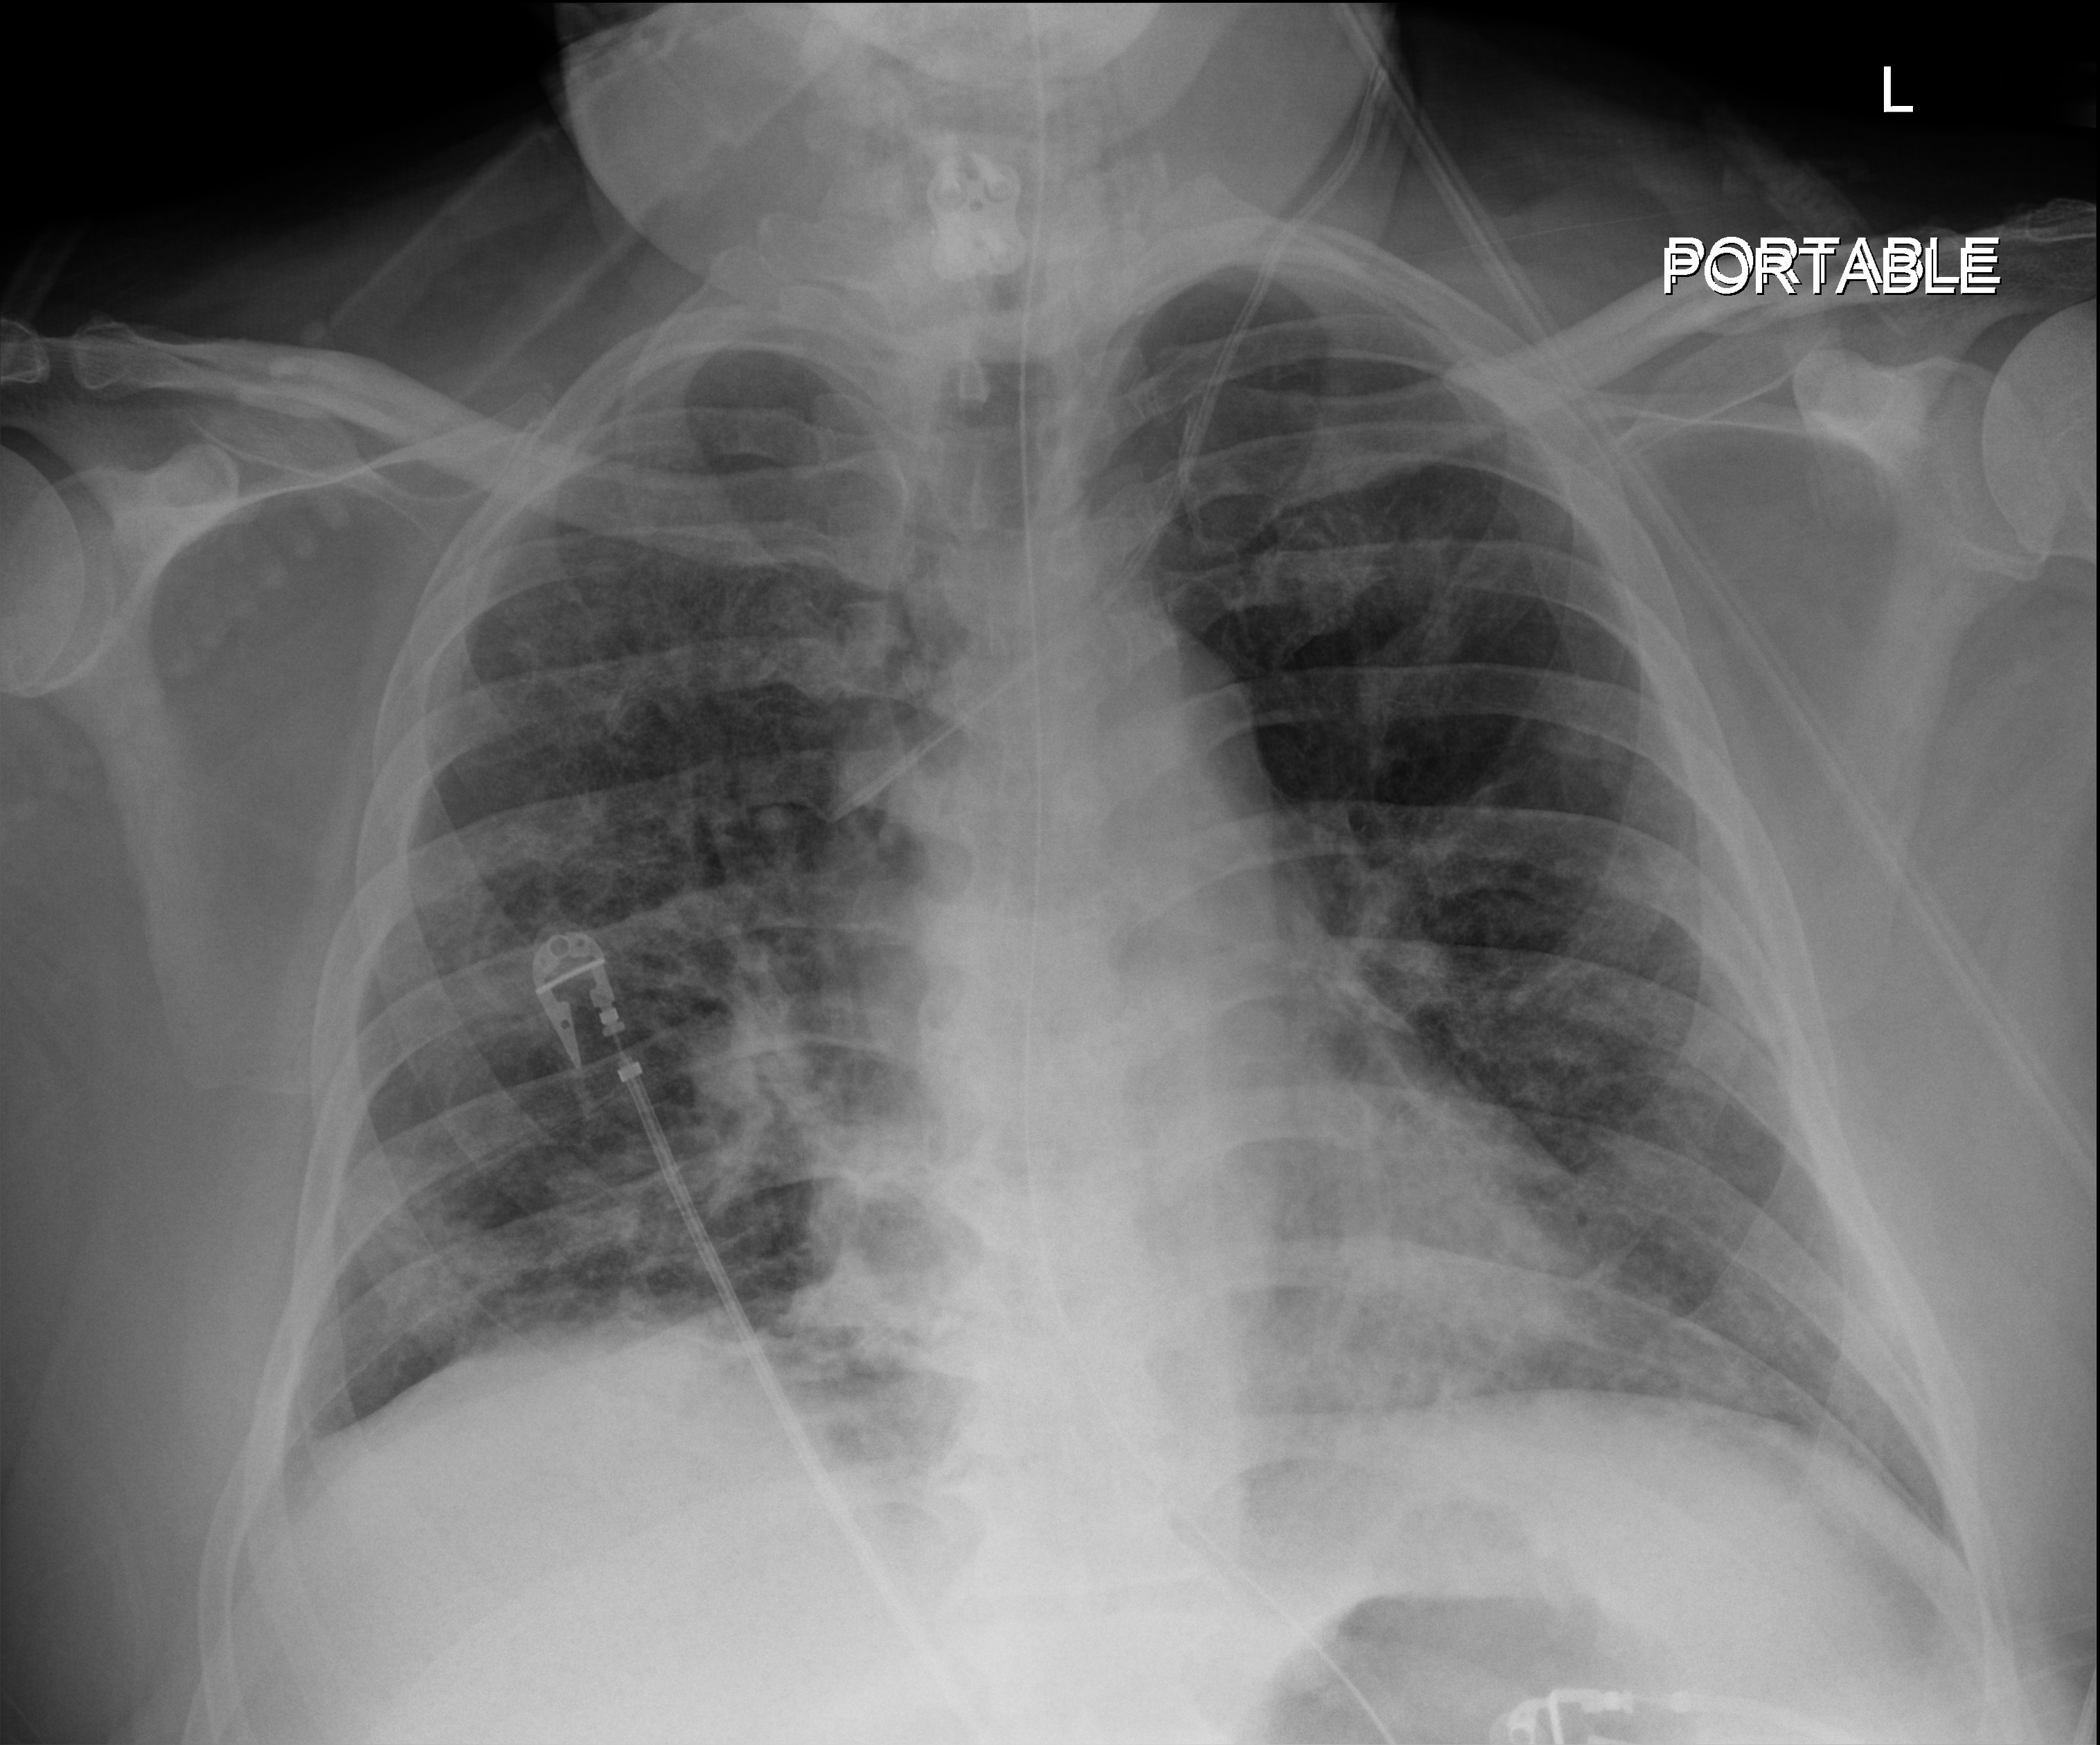
Chest X-ray (portable). Male patient hospitalised with COVID-19, age 18–59 years.
From the hospital-stay record, not from the radiograph (when in the stay this image was taken is not recorded): mechanically ventilated during this hospital stay: yes; chronic kidney disease (admission record): no; admitted to intensive care during this hospital stay: yes.